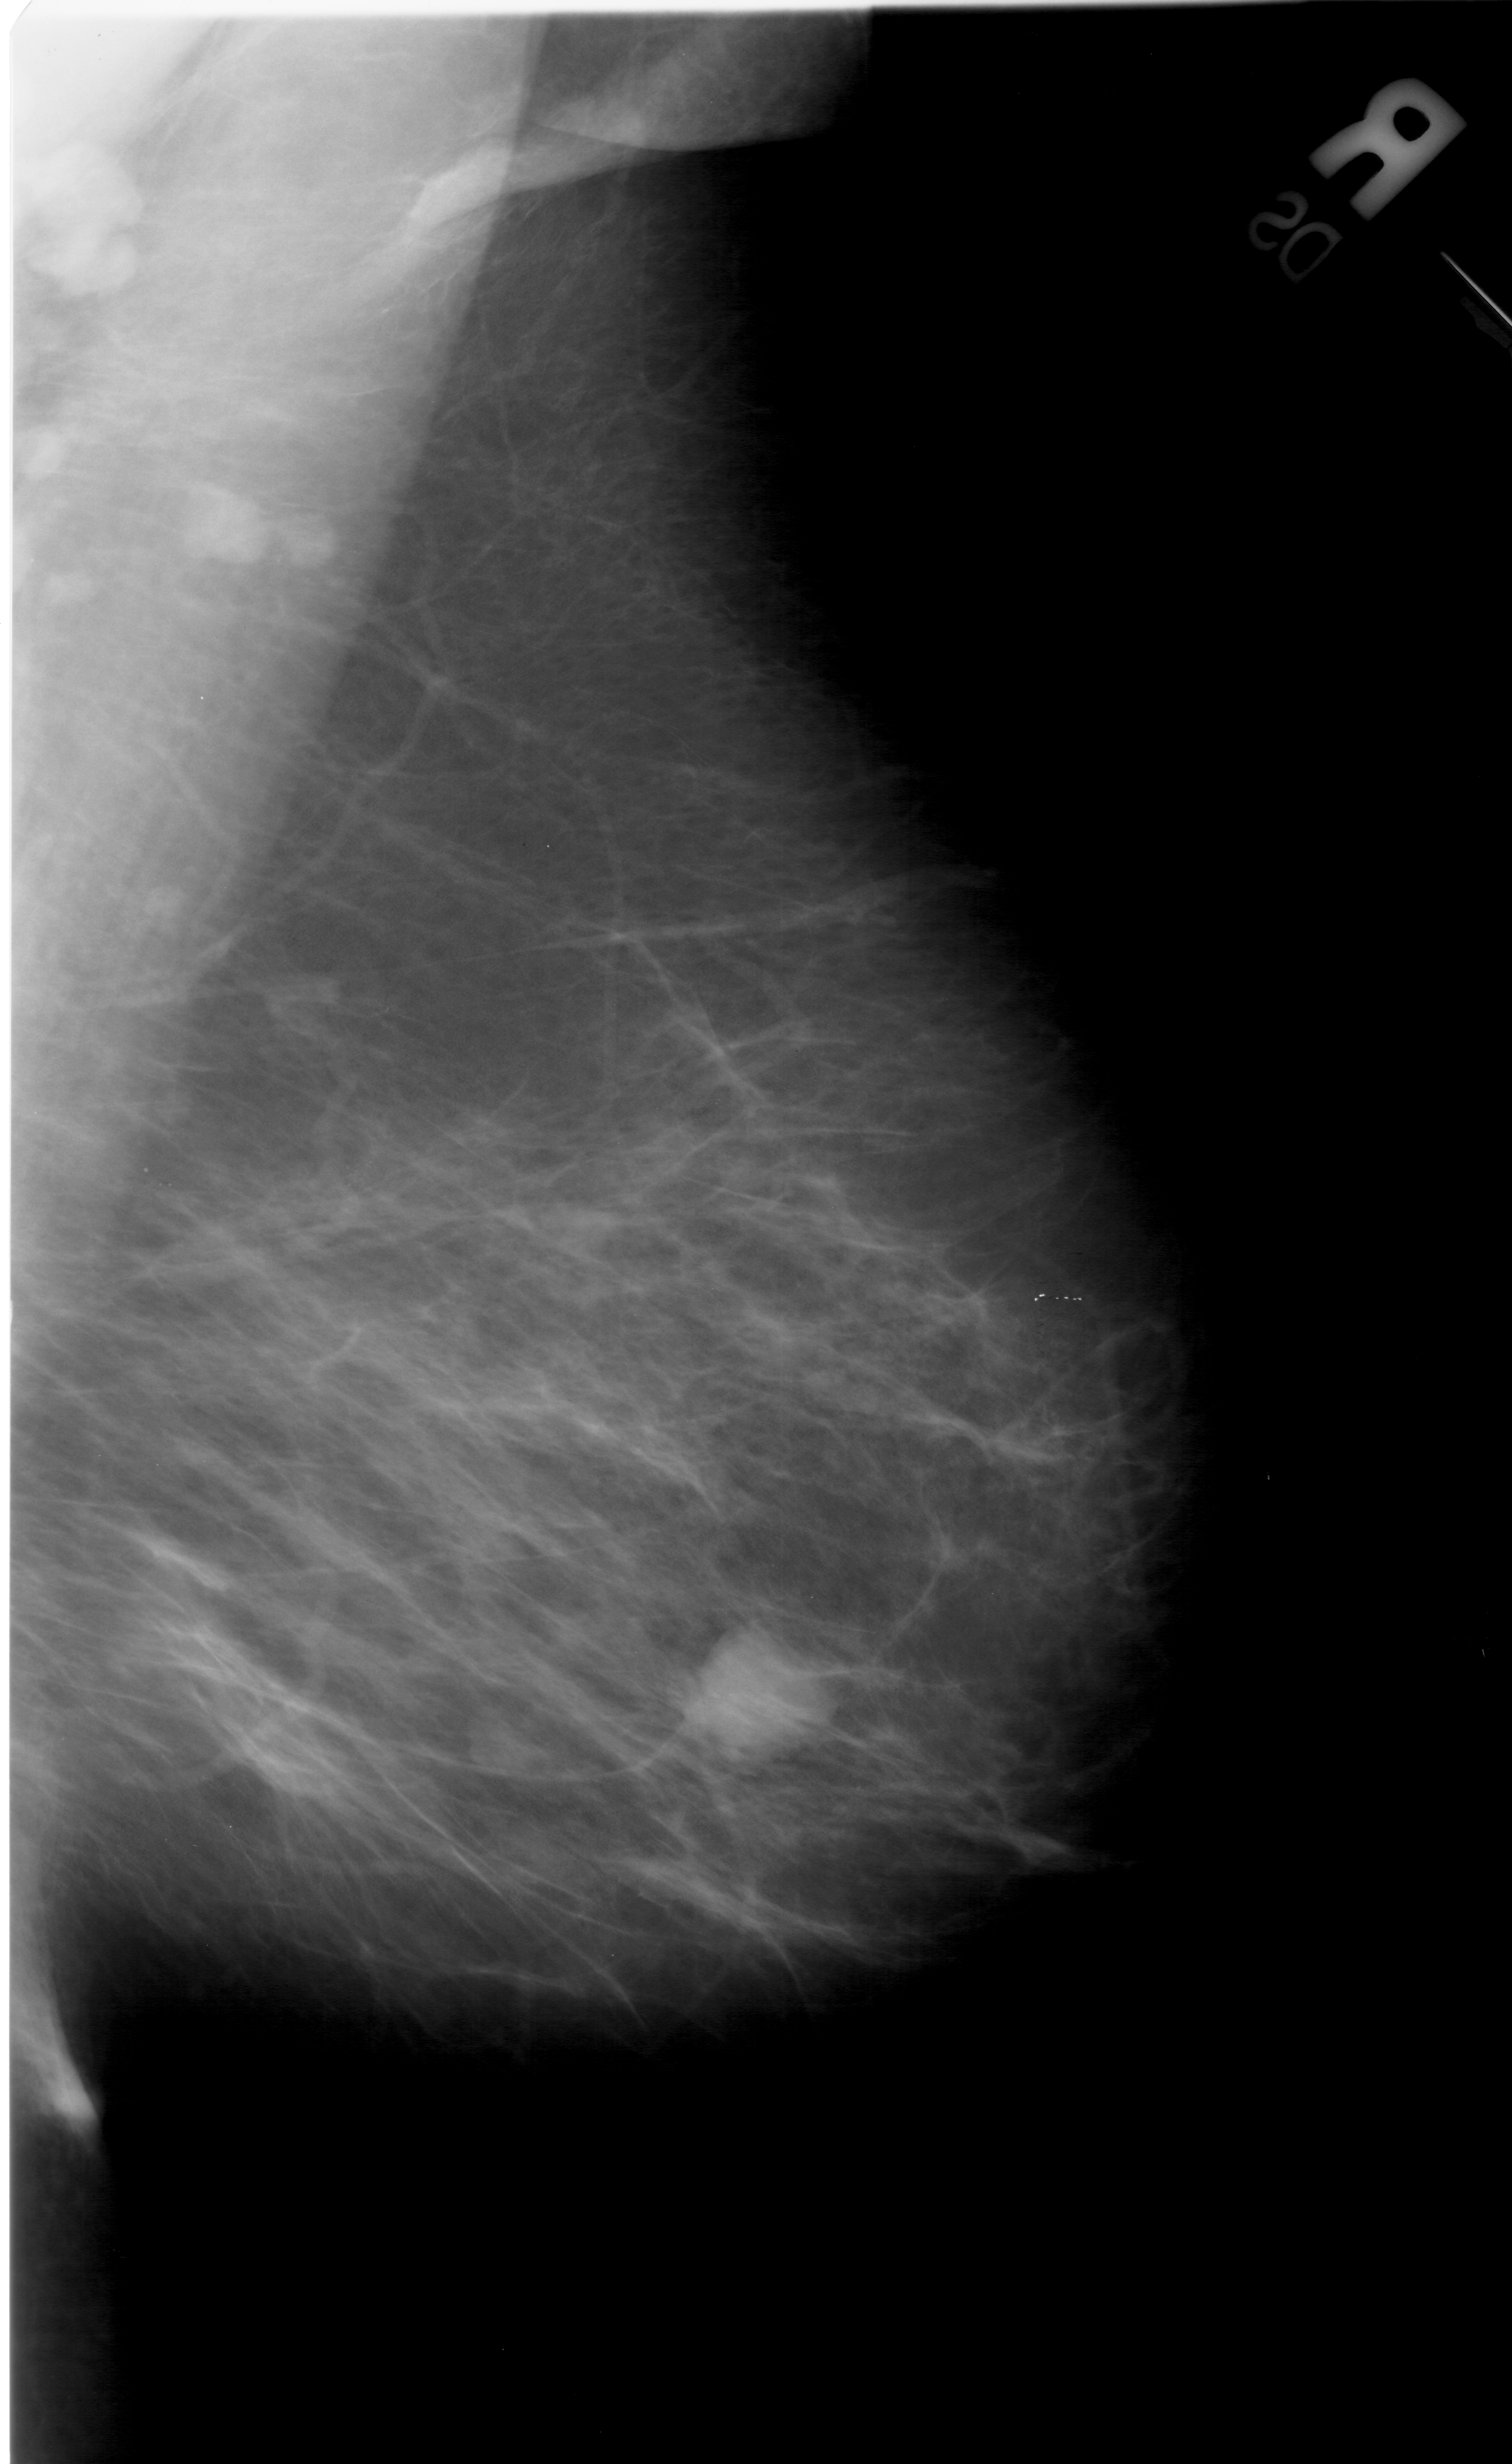
Digitized screen-film mammogram. Right breast. MLO view. Breast composition: heterogeneously dense (BI-RADS density category 3 of 4). 1512 × 2464 image matrix.
Marked abnormalities (boxes around the expert regions of interest):
- mass, shape lobulated, margins circumscribed; BI-RADS assessment category 4; subtlety rating 5 on a 1 (subtle) to 5 (obvious) scale; pathology (as recorded): benign: bounding box <695,1614,855,1758> (left, top, right, bottom; pixels)